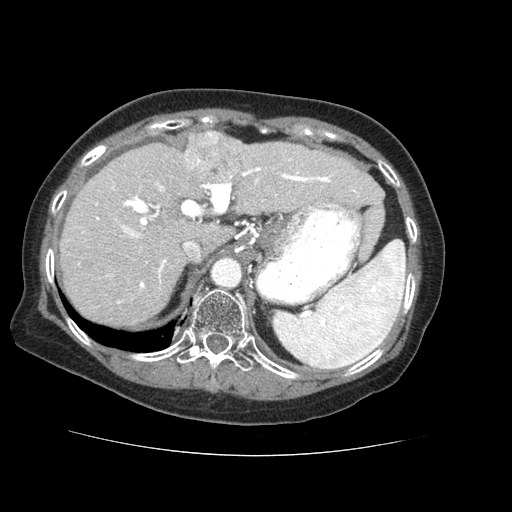
Contrast-enhanced abdominal CT (liver protocol), one axial slice. Position 45 of 73 along the scan axis. Reconstruction kernel STANDARD. 120 kVp. Soft-tissue window (W 400 / L 40 HU). 512 × 512 image matrix, field of view 360 × 360 mm. Case-level facts recorded for this patient, not image findings: diagnosis: hepatocellular carcinoma (patient treated with transarterial chemoembolisation; whether this scan precedes or follows treatment is not stated here); TNM stage (as recorded): Stage-IVB; Child-Pugh class: A; tumour differentiation: well differentiated; tumour nodularity: uninodular.
Outlined on this slice (semi-automatic segmentation, software-assisted and operator-edited):
- liver parenchyma outside the tumour (the mass and vessels are separate outlines, so this box may not span the whole liver): bounding box (x1, y1, x2, y2) in pixels: (60, 130, 382, 326)
- mass: (183, 130, 244, 182)
- liver vessels: (96, 159, 359, 304)